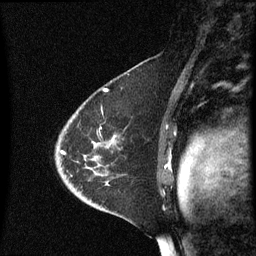
Breast MRI (dynamic contrast-enhanced), one sagittal slice; position 41 of 60 along the scan axis; dynamic contrast-enhanced series, image 2 of 3 at this slice position (ordered by acquisition); 1.5 T; TE 4.2 ms, TR 8.4 ms; 2.3 mm slice thickness; 256 × 256 image matrix, field of view 200 × 200 mm. Female patient, age 46 years. Case-level facts recorded for this patient, not image findings: setting: breast cancer imaged before/during neoadjuvant chemotherapy; receptor status: HER2-positive.
Outlined on this slice (semi-automatic segmentation, software-assisted and operator-edited):
- analysis volume of interest (the breast-tissue region the enhancement analysis was run in; not a lesion): bounding box (x1, y1, x2, y2) in pixels: (56, 100, 166, 187)
- tumour enhancement mask (voxels above the 70 % enhancement threshold inside the analysis volume of interest): (61, 152, 64, 155)